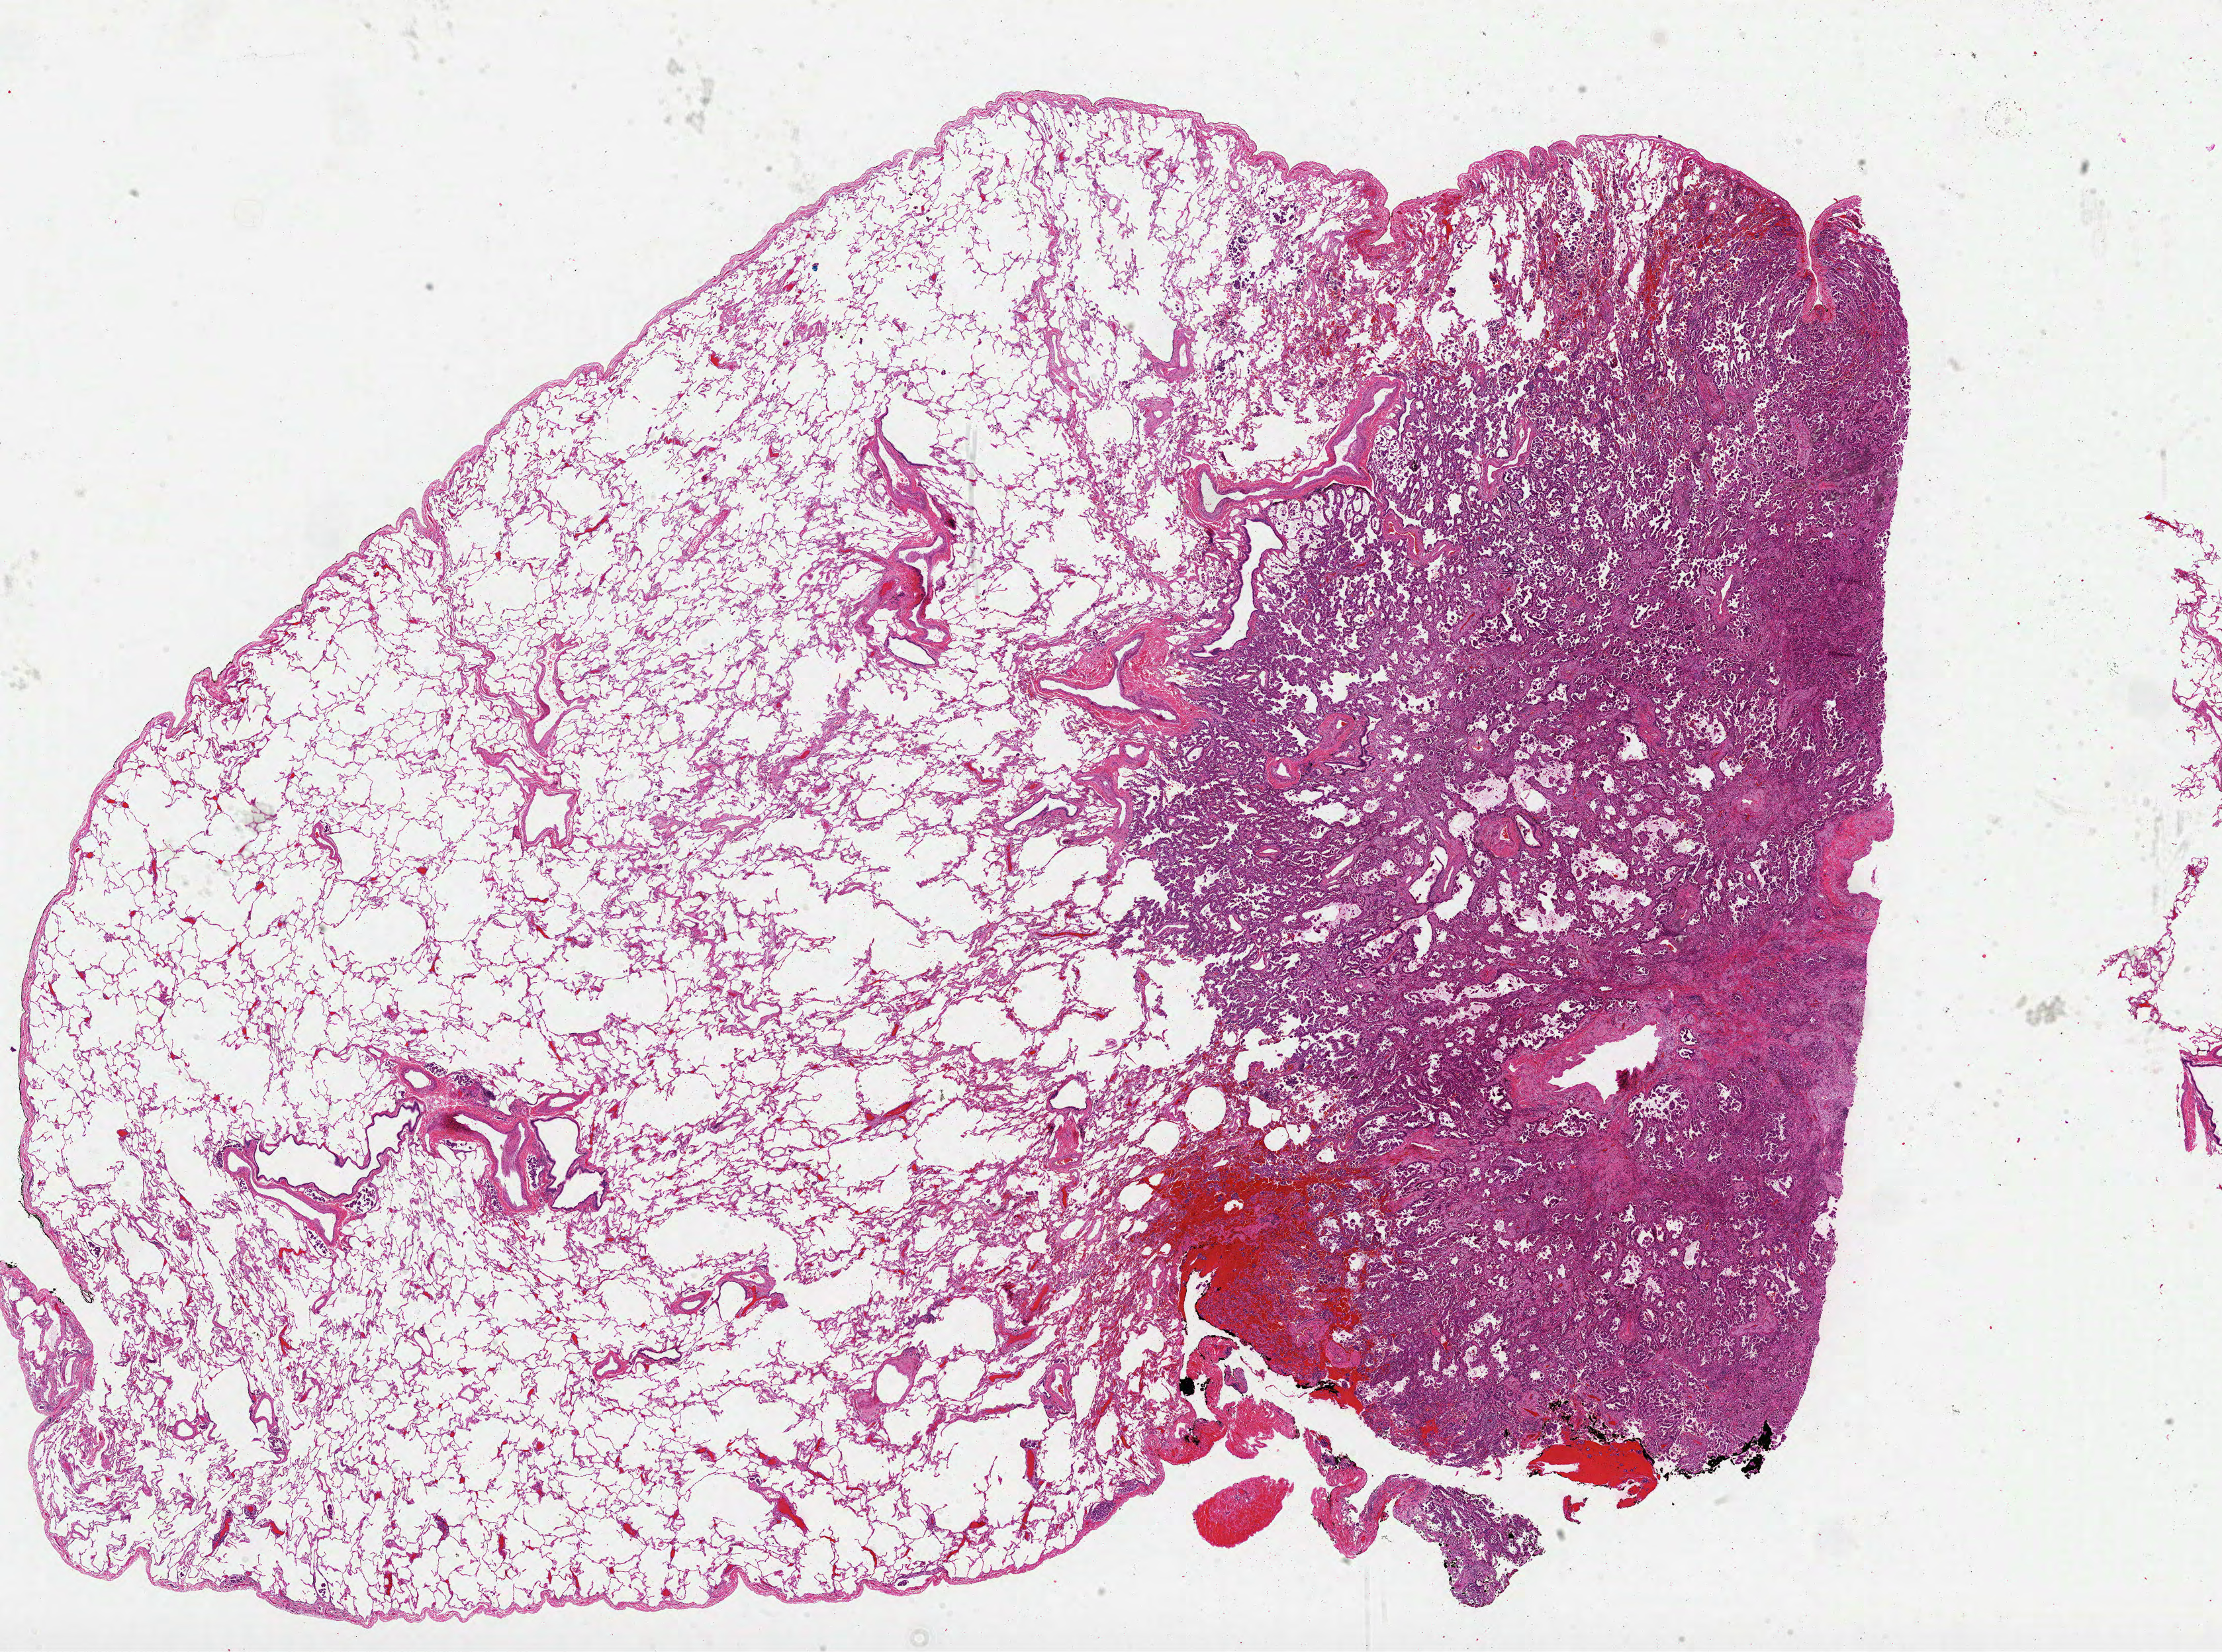
Digitized H&E tissue section (whole slide) — low-resolution overview of the scanned area, about 27.1 x 20.1 mm; formalin-fixed paraffin-embedded (FFPE) diagnostic section; lung, primary tumour sample. Female patient; age at initial diagnosis 69 years.
* diagnosis: Adenocarcinoma, NOS (middle lobe, lung)
* AJCC pathologic stage: IIIA (6th edition)